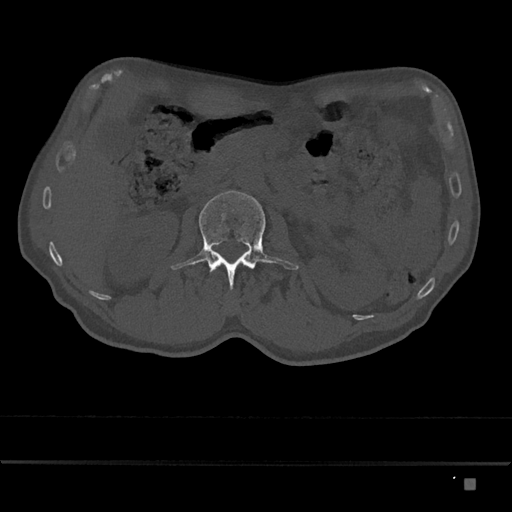
CT including the spine, one axial slice; slice 480 of 797 in the series (ordered by position); reconstruction kernel Br40s/3; 120 kVp; bone window (W 1800 / L 400 HU); 512 × 512 image matrix, field of view 390 × 390 mm. Male patient, age 72 years. Case-level facts recorded for this patient, not image findings: primary cancer: prostate.
Structures marked on this image (semi-automatically segmented with operator editing):
- L2 vertebra: bounding box <171,191,299,289> (left, top, right, bottom; pixels)